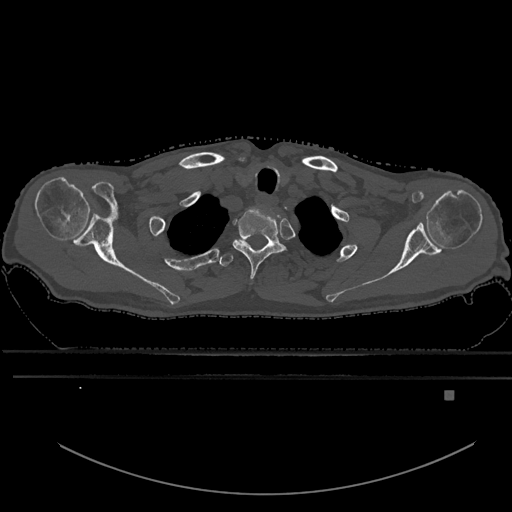
CT including the spine, one axial slice; slice 531 of 969 in the series (ordered by position); bone window (W 1800 / L 400 HU); 0.5 mm slice thickness; 512 × 512 image matrix. Male patient, age 82 years. Case-level facts recorded for this patient, not image findings: primary cancer: prostate.
Structures marked on this image (semi-automatic segmentation, software-assisted and operator-edited):
- T1 vertebra: bounding box [x1, y1, x2, y2] px = [232, 208, 284, 280]
- T2 vertebra: [219, 239, 279, 267]